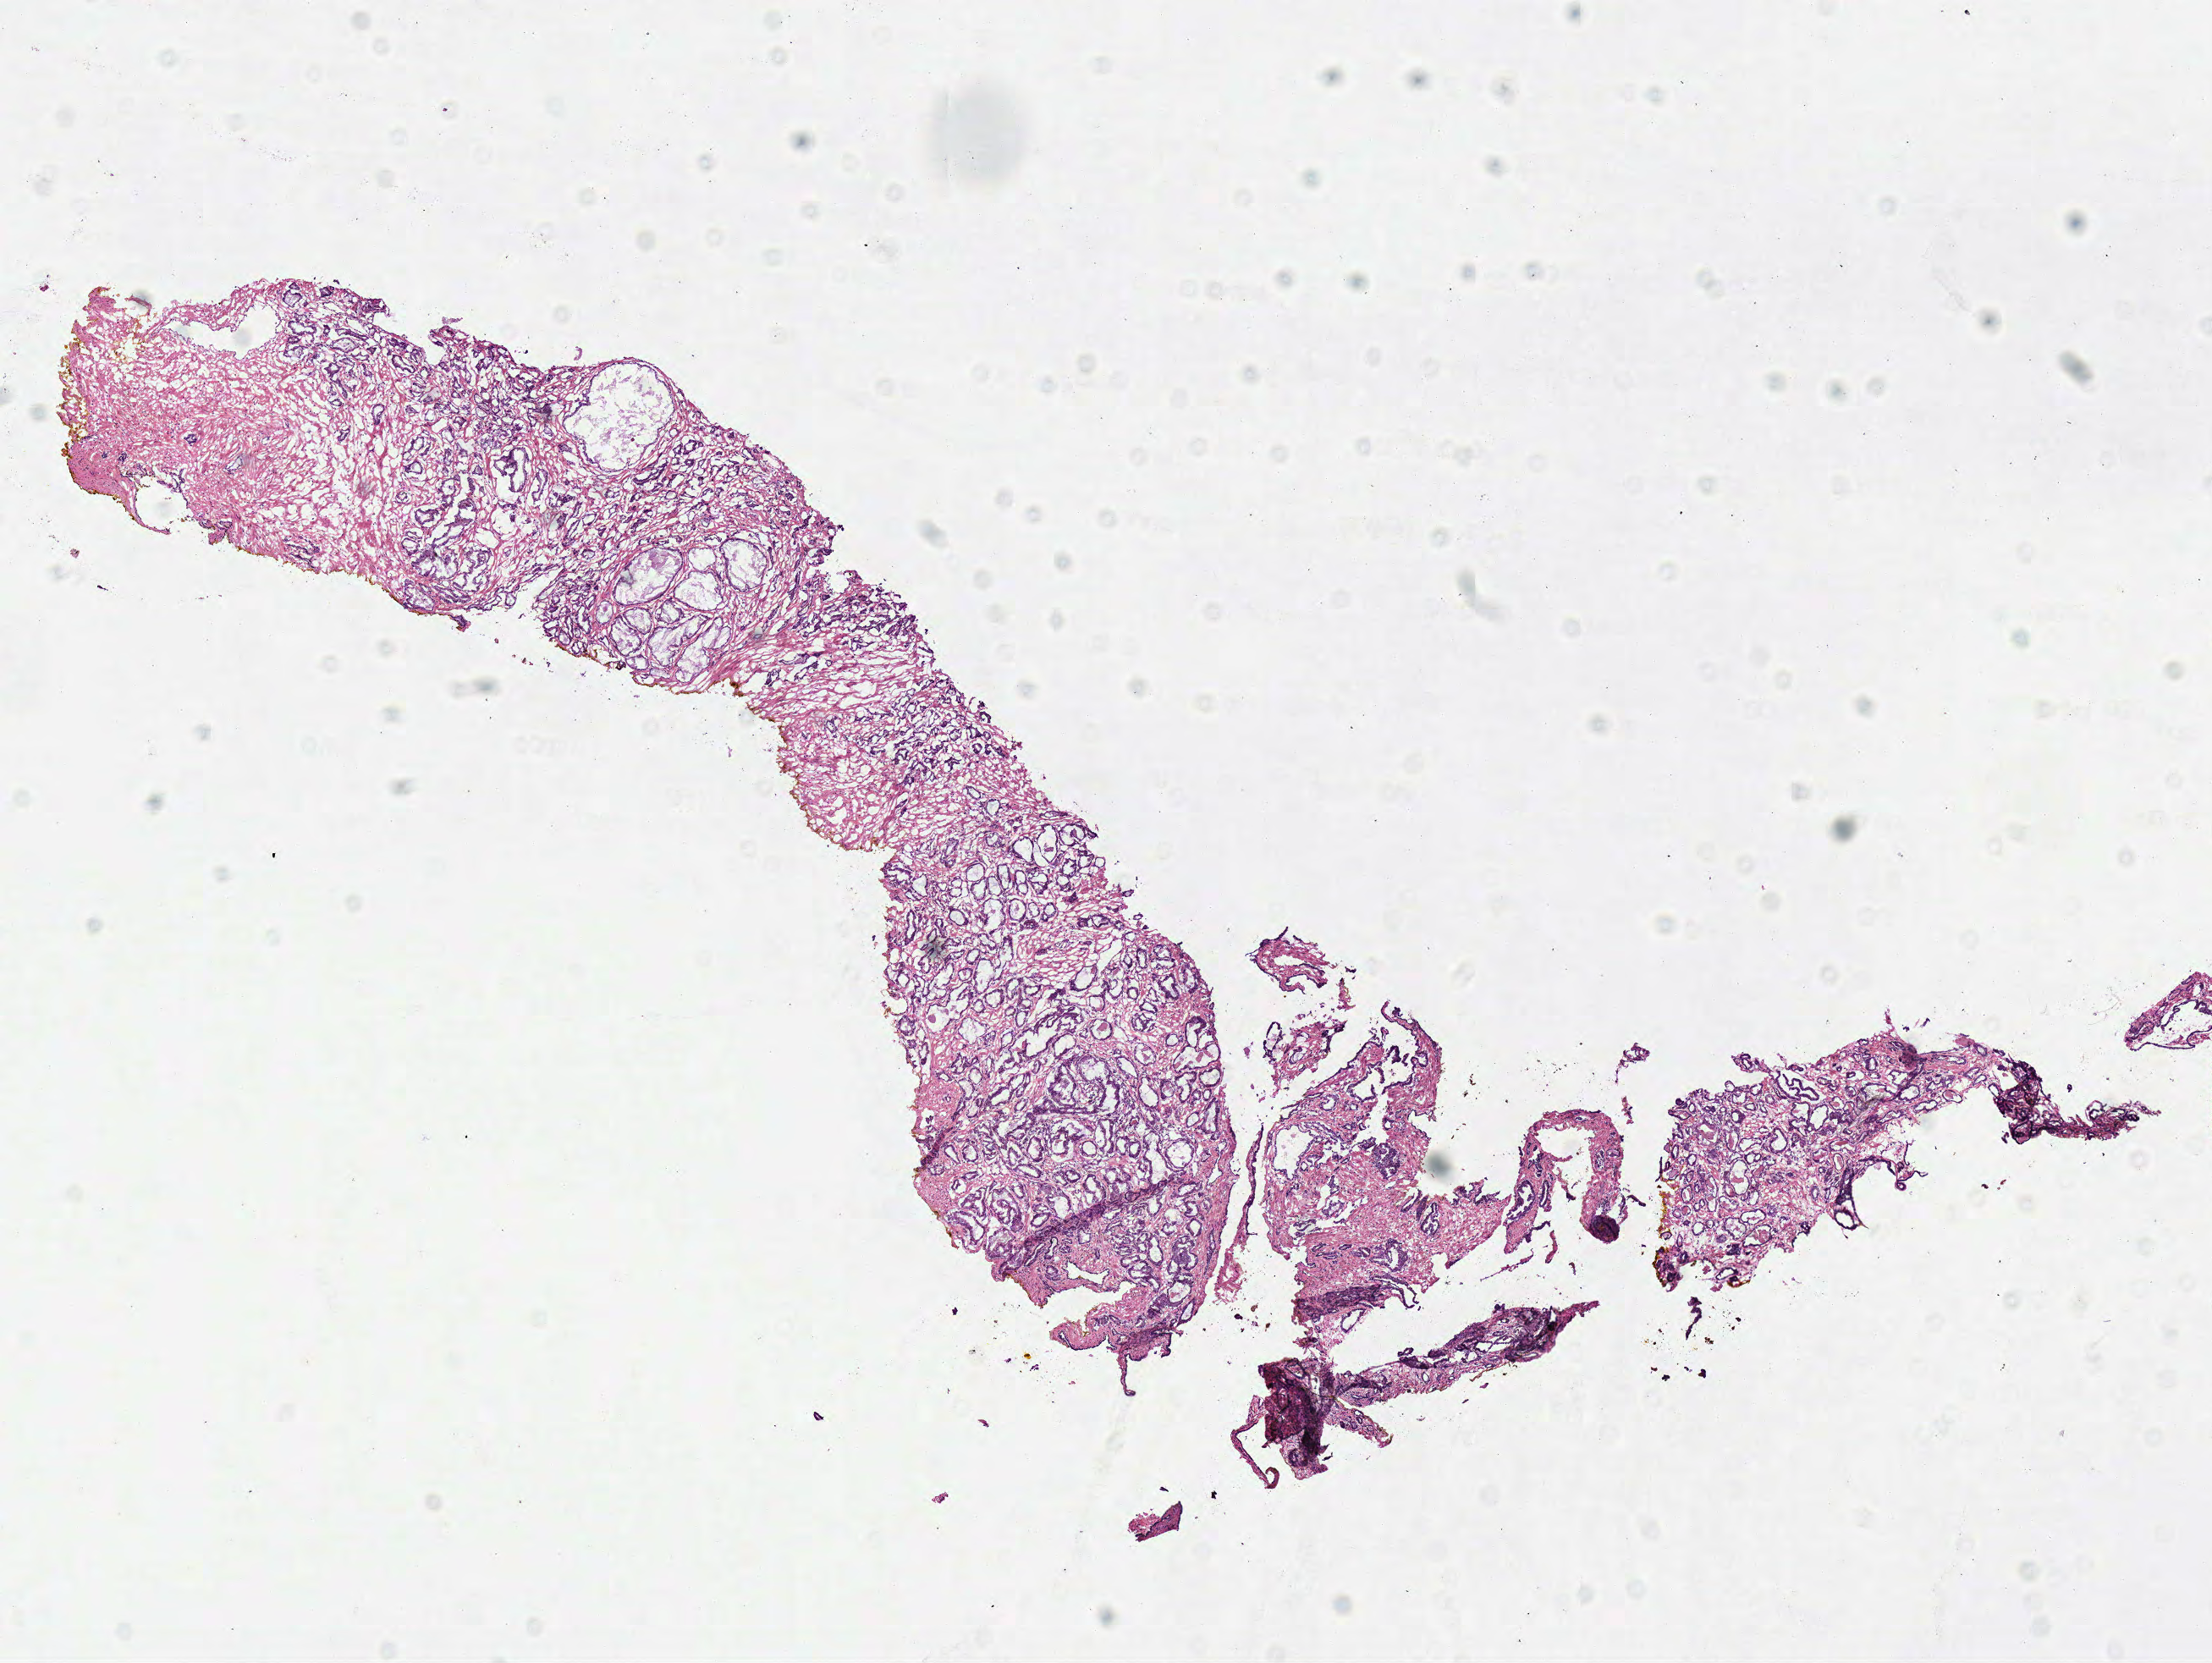
Digitized Hematoxylin and eosin (H&E) stained tissue section (whole slide), a low-resolution overview of the entire scanned area, about 10.3 x 7.7 mm, frozen section from the top of the tissue portion, primary tumour sample from the prostate. Male, age 58 years at initial diagnosis. Gleason score: 6 (3+3). Composition of this section per pathologist review: tumour cells 60%, tumour nuclei 60%, normal cells 20%, stromal cells 20%, necrosis 0%. Infiltration values recorded for this section: lymphocyte infiltration 2%, monocyte infiltration 0%, neutrophil infiltration 0%.
* pathologic diagnosis: Acinar cell carcinoma (prostate gland)
* laterality: bilateral